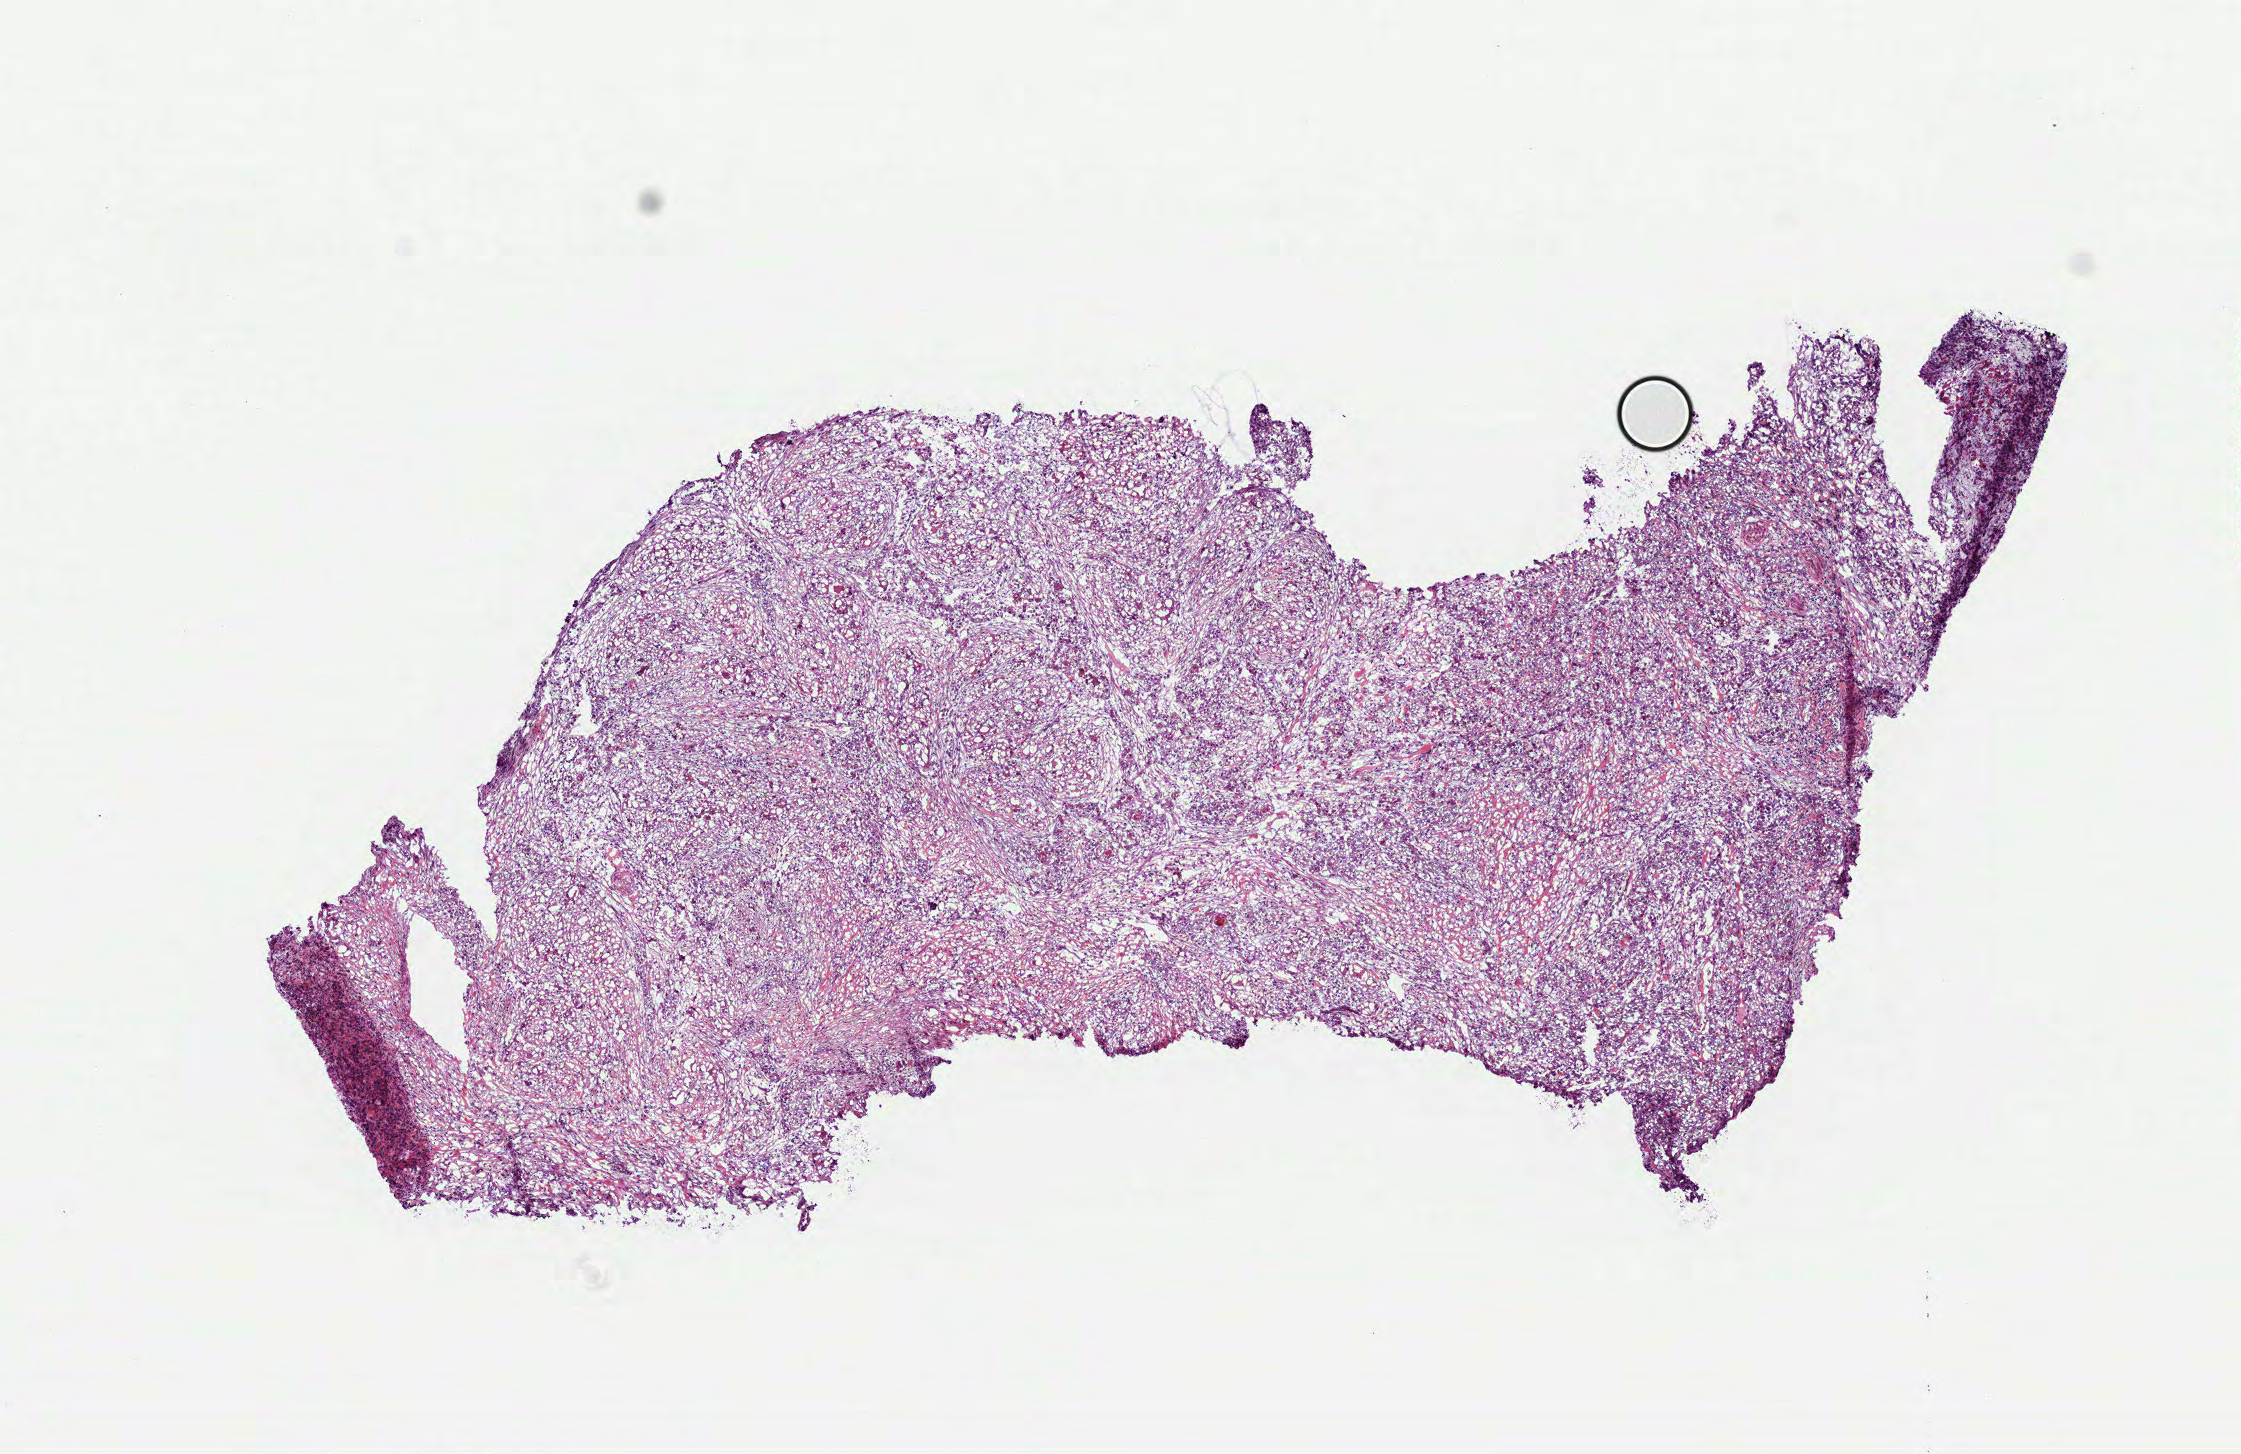
Whole-slide histology image, H&E-stained — whole scanned area (about 9.0 x 5.9 mm) shown as a low-resolution overview. Frozen section. Sample: primary tumour, head and neck. Male patient; age at initial diagnosis 52 years. Histologic grade: G3 (poorly differentiated). Composition of this section per pathologist review: tumour cells 90%, tumour nuclei 85%, normal cells 0%, stromal cells 10%, necrosis 0%.
* lymph nodes positive (case pathology): 3 of 29 examined
* diagnosis: Squamous cell carcinoma, NOS (tongue, NOS)
* laterality: left
* AJCC pathologic stage: IVA (6th edition)